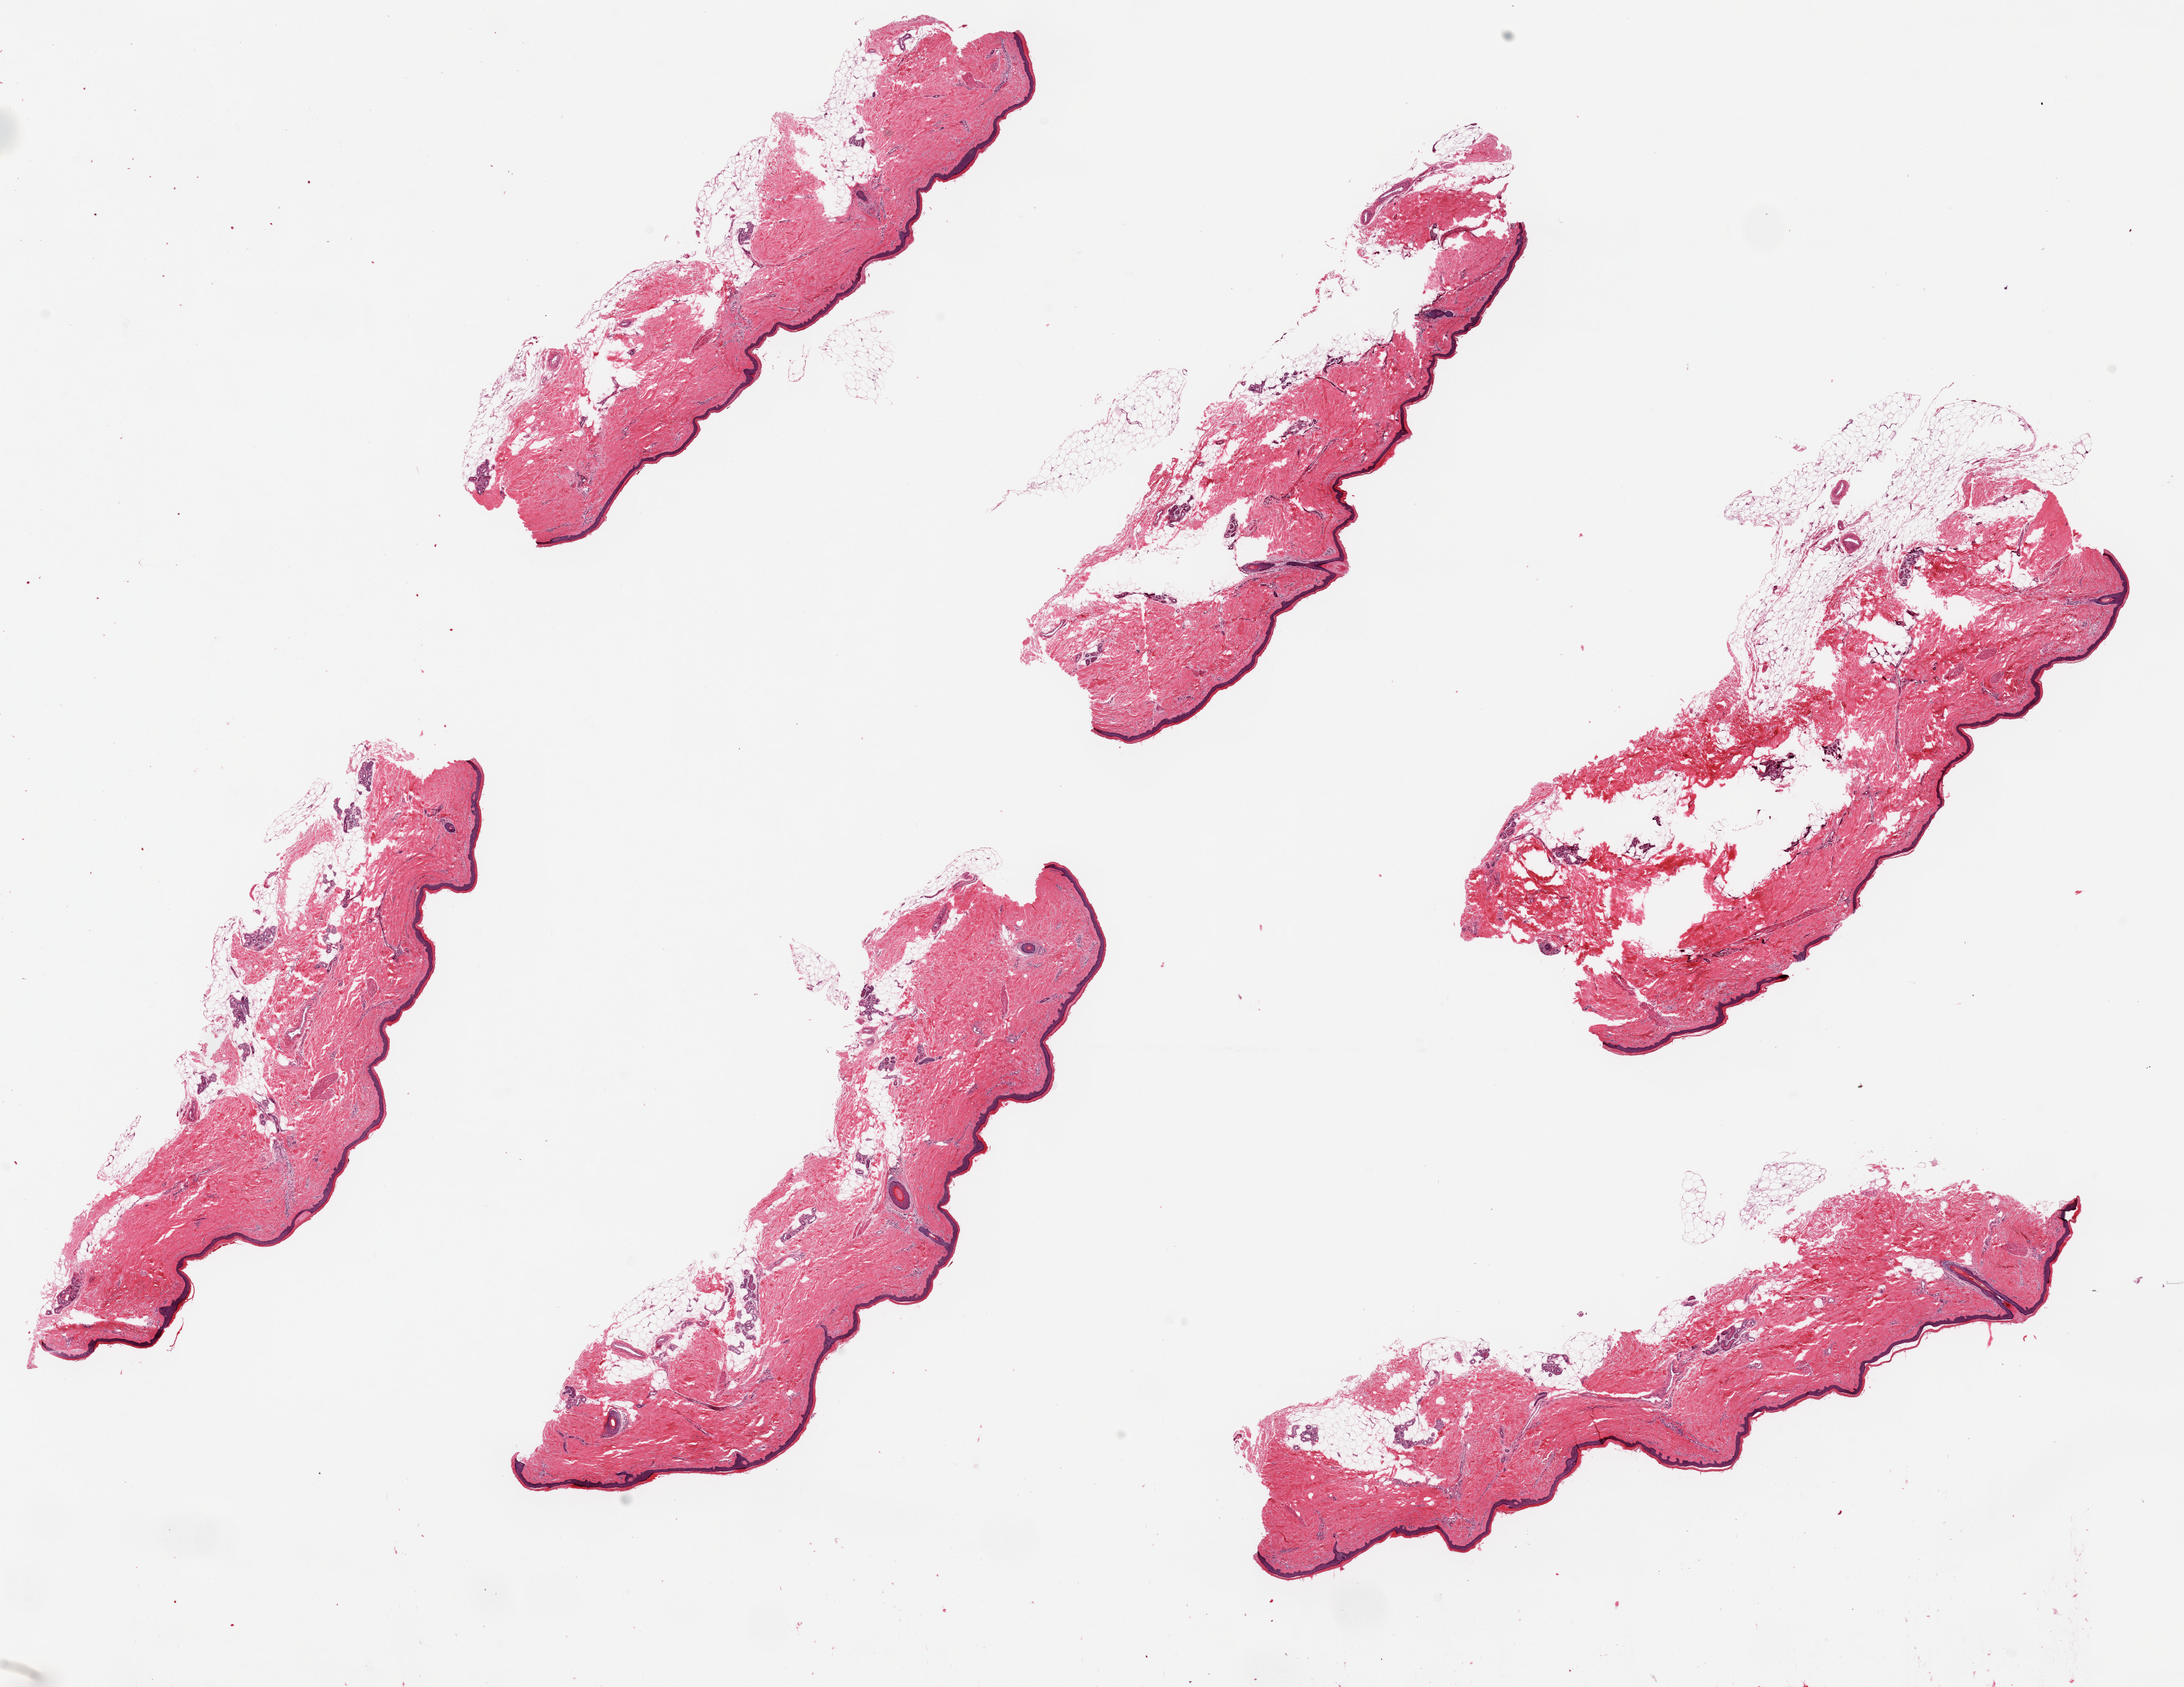
Whole-slide image, haematoxylin and eosin stain, whole scanned area (about 23.6 x 18.2 mm, from a 20x scan) shown as a low-resolution overview, PAXgene-fixed, paraffin-embedded tissue, sampled site (target tissue): skin of lower leg, tissue donor sample. Donor: female.
• review note (as recorded): 6 pieces, up to 10x3mm; sqaumous epithilum is ~2% thickness